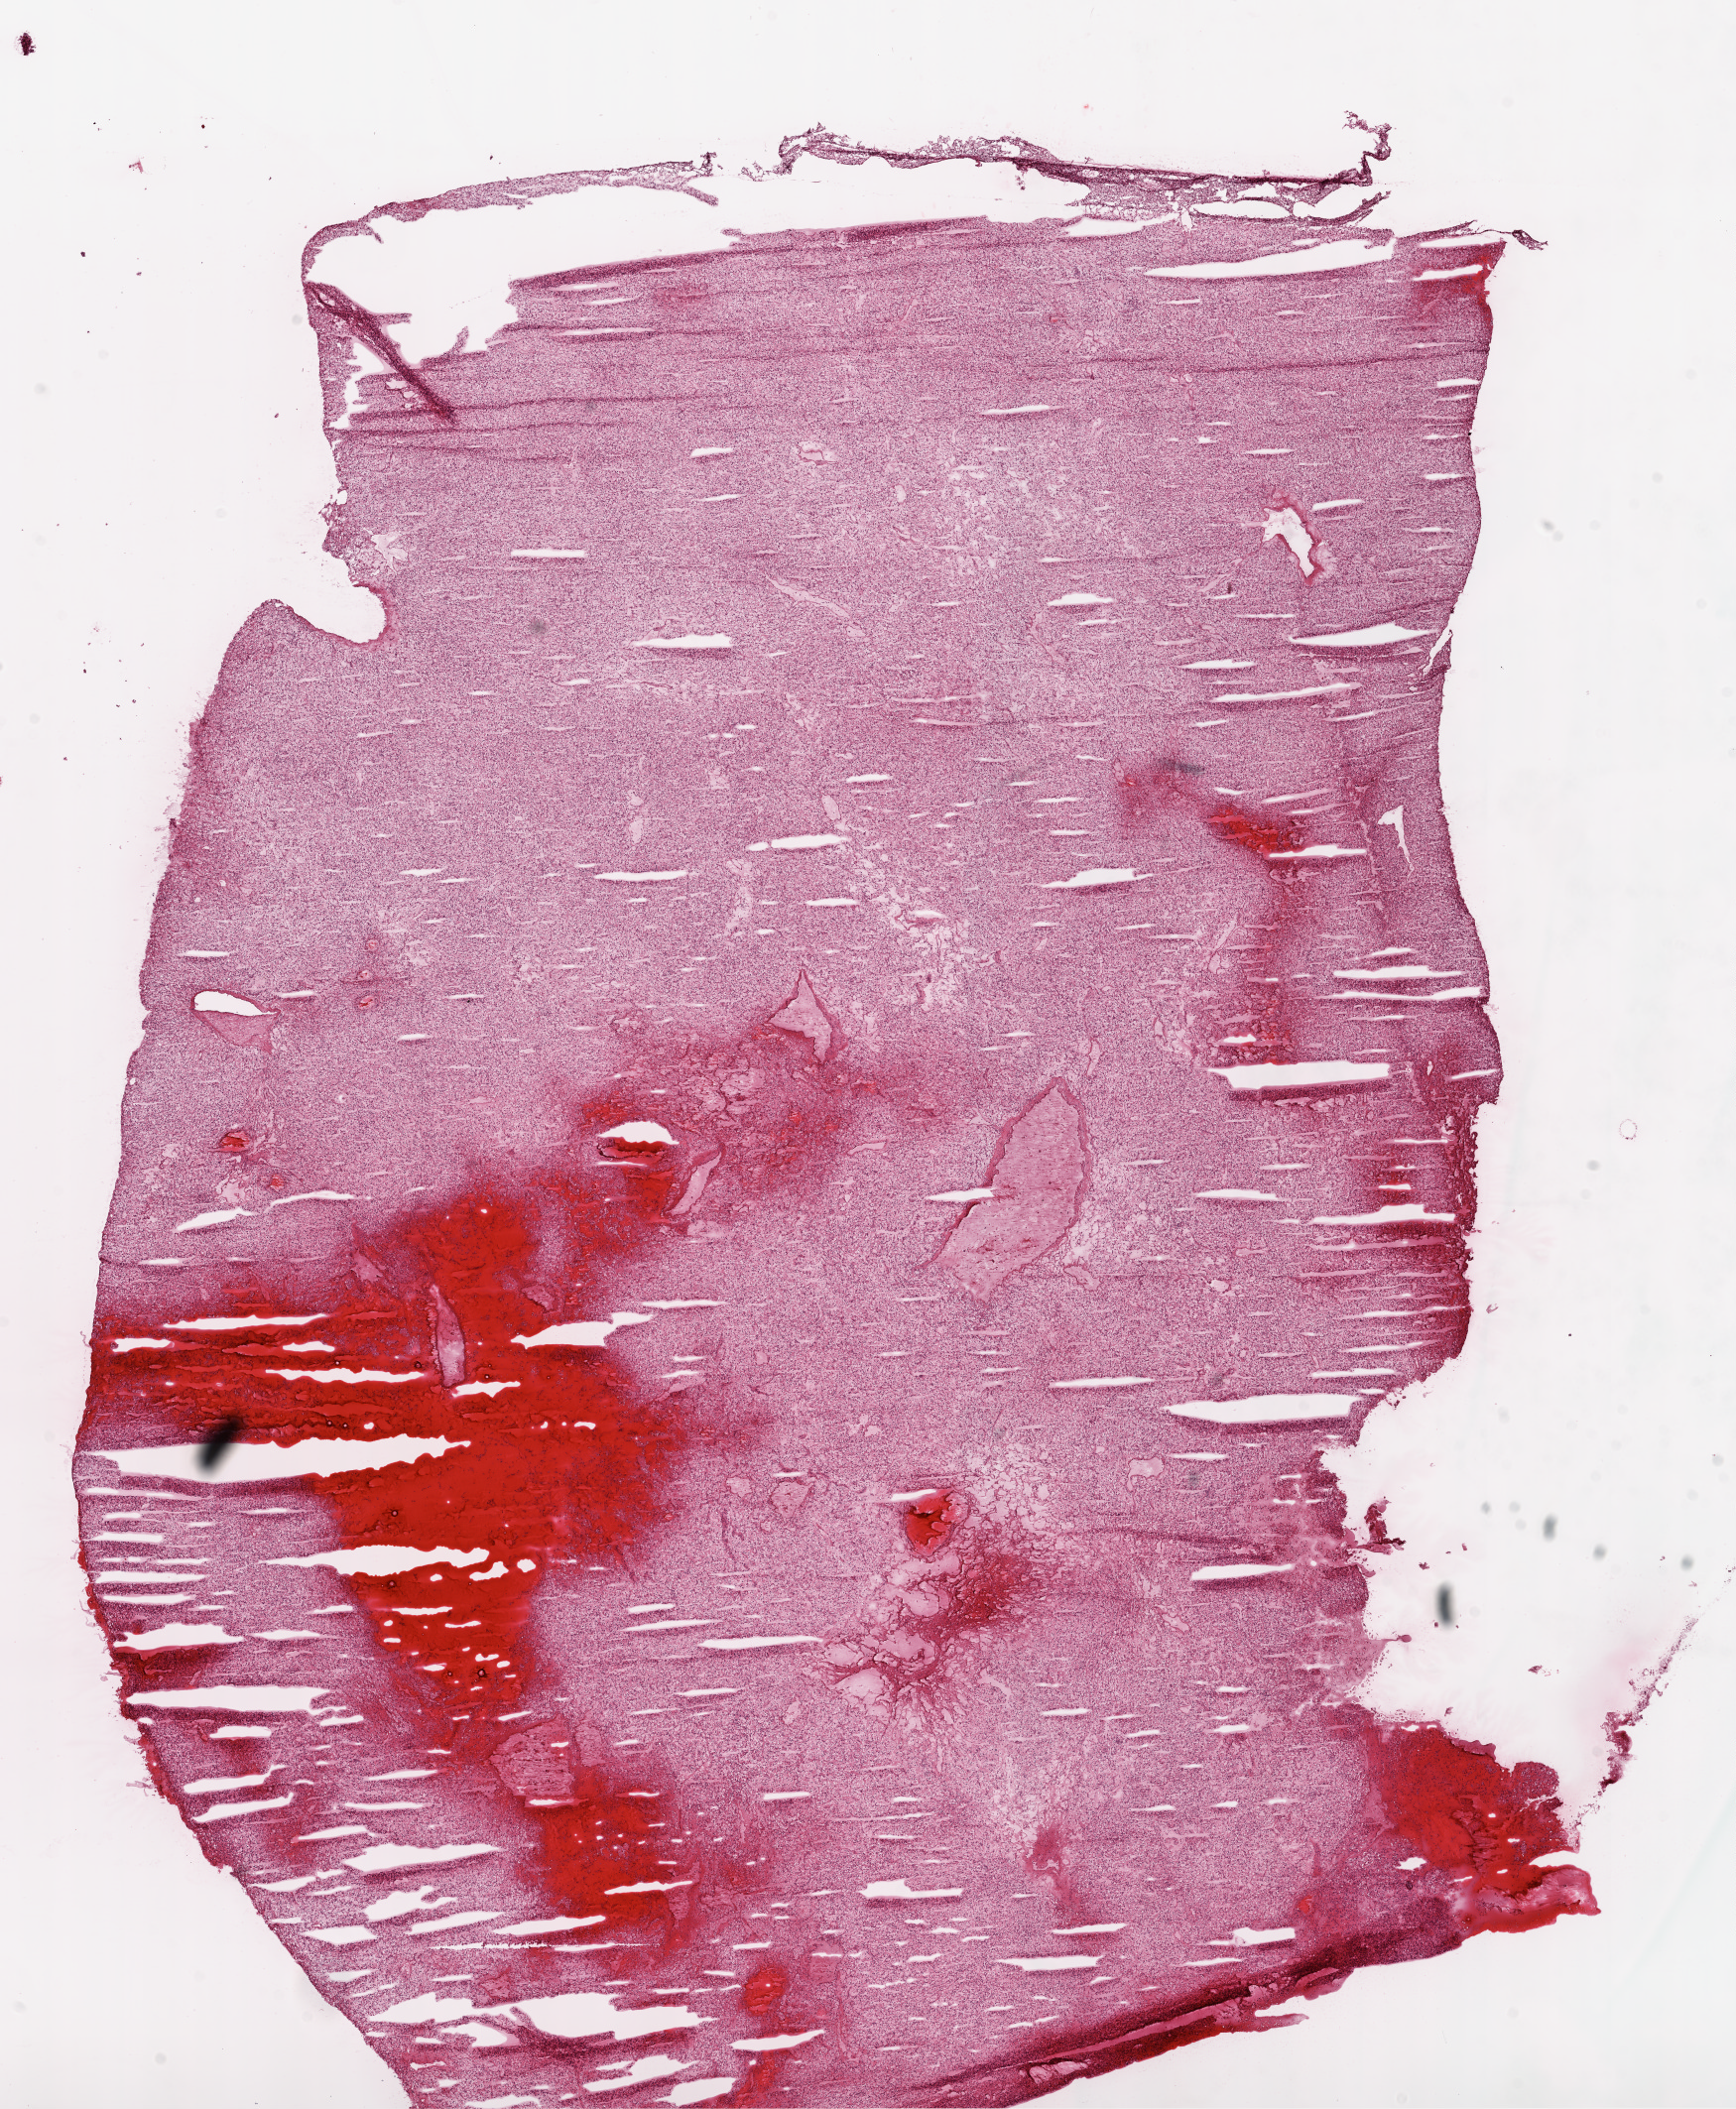
Whole-slide histology image, H&E-stained, shown as a low-resolution overview of the whole scanned area (about 14.0 x 17.1 mm), frozen section, kidney, primary tumour sample. Patient: female, age at initial diagnosis 57 years.
Histologic diagnosis: Clear cell adenocarcinoma, NOS.